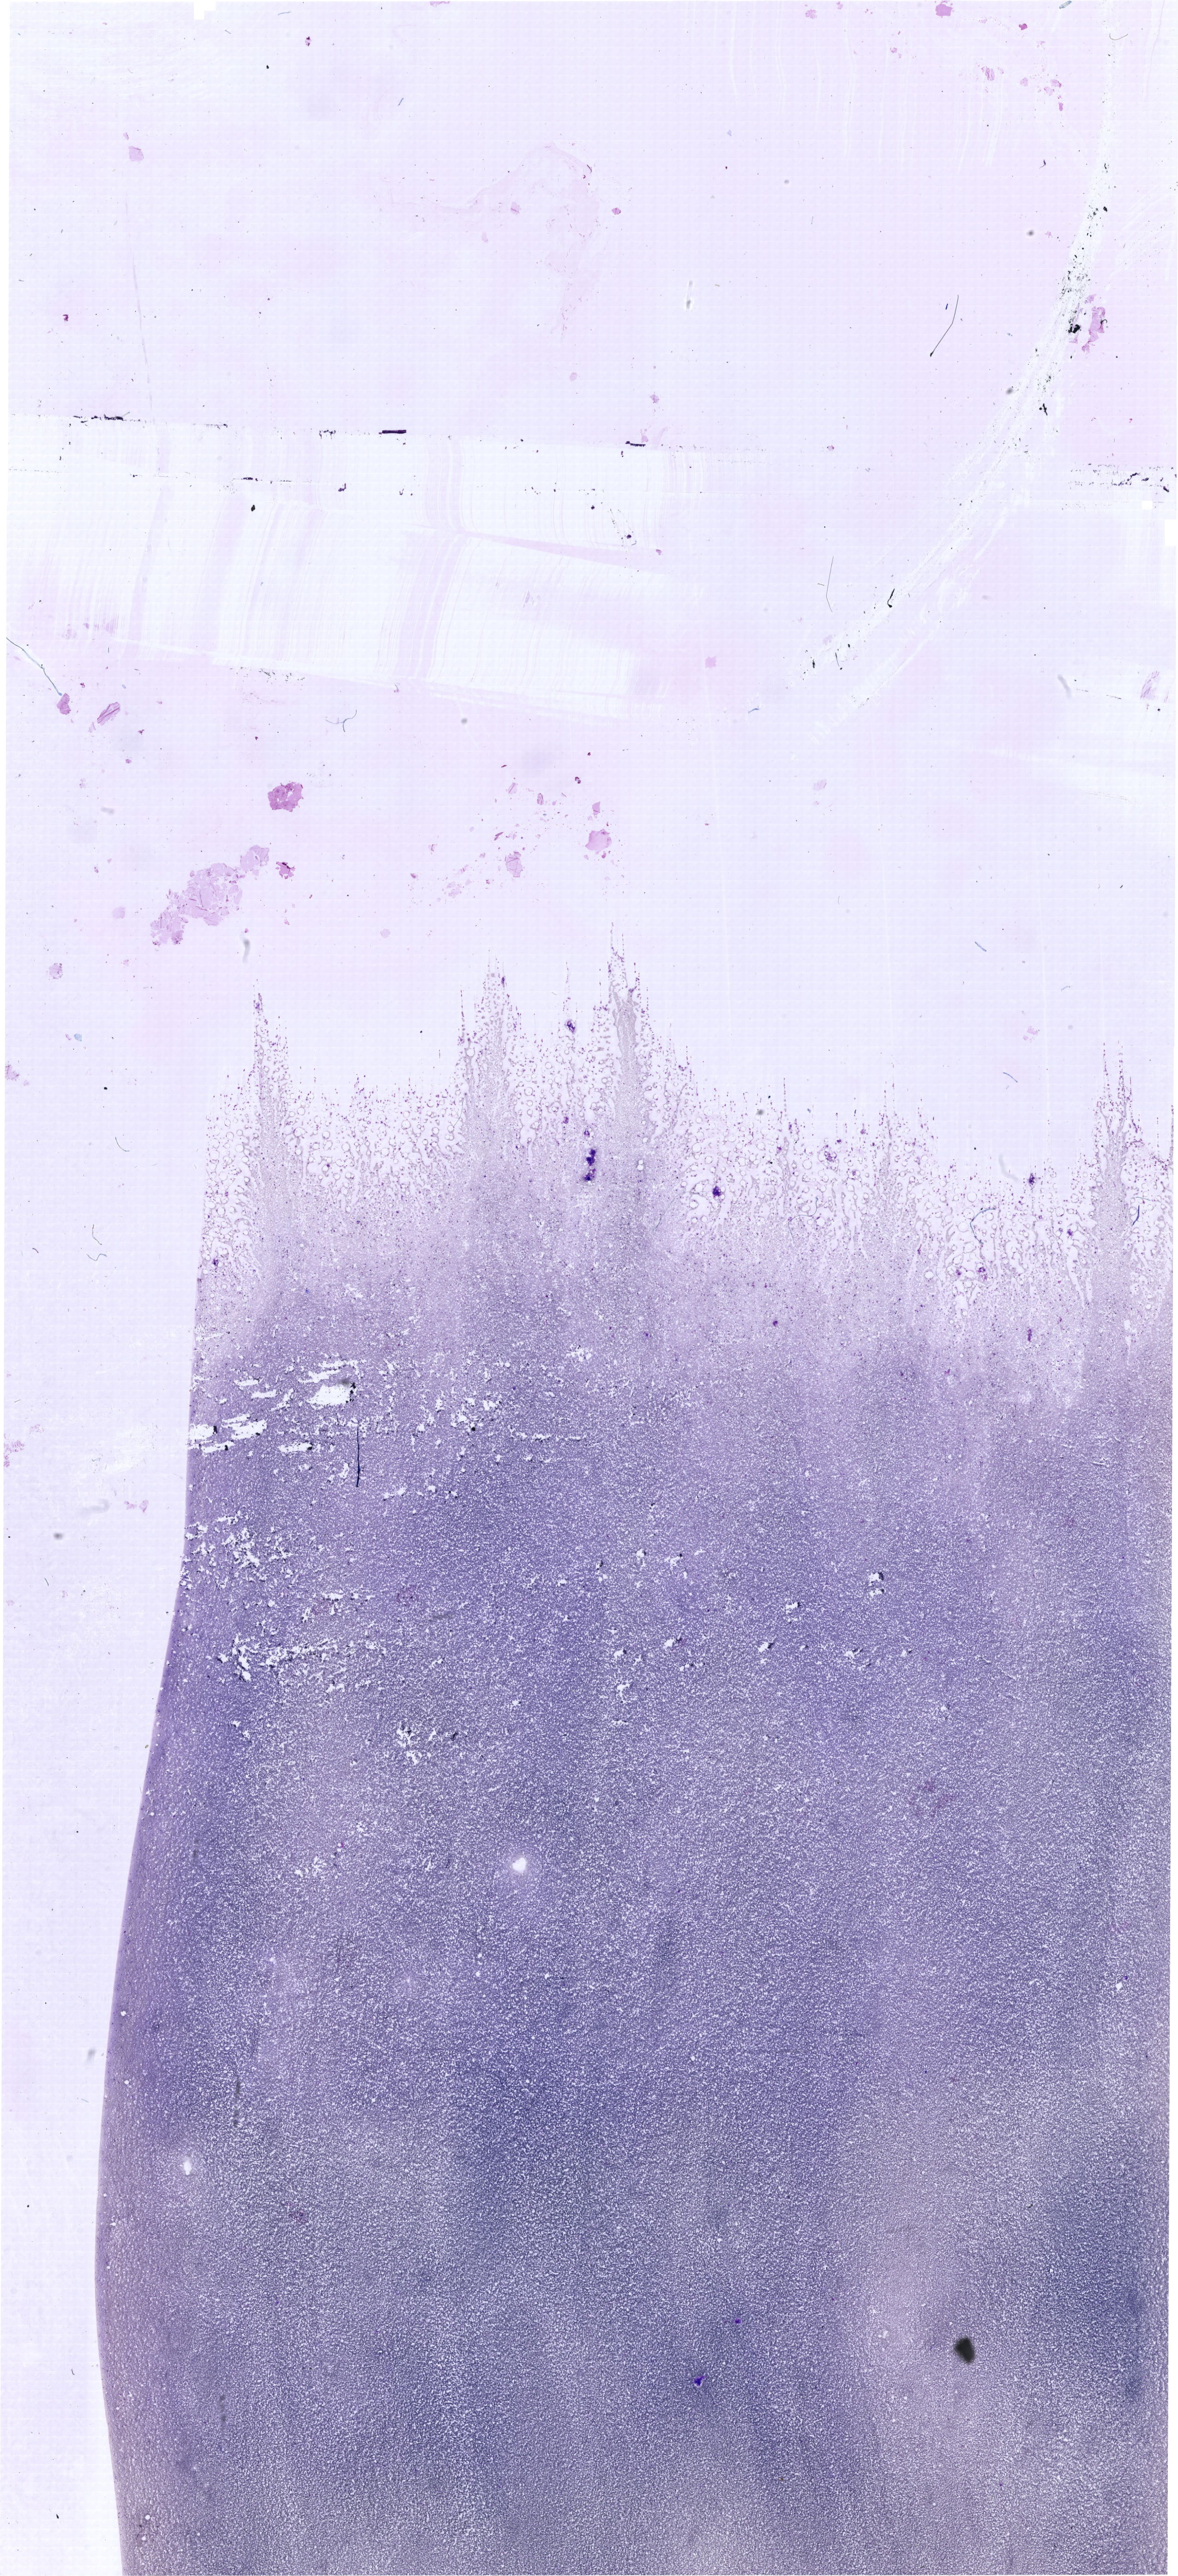
Whole-slide image of a May-Grünwald–Giemsa-stained bone marrow aspirate smear — low-resolution overview of the scanned area, about 19.9 x 43.6 mm. Patient sex: female.
• diagnosis: Mixed Phenotype Acute Leukemia, B/Myeloid